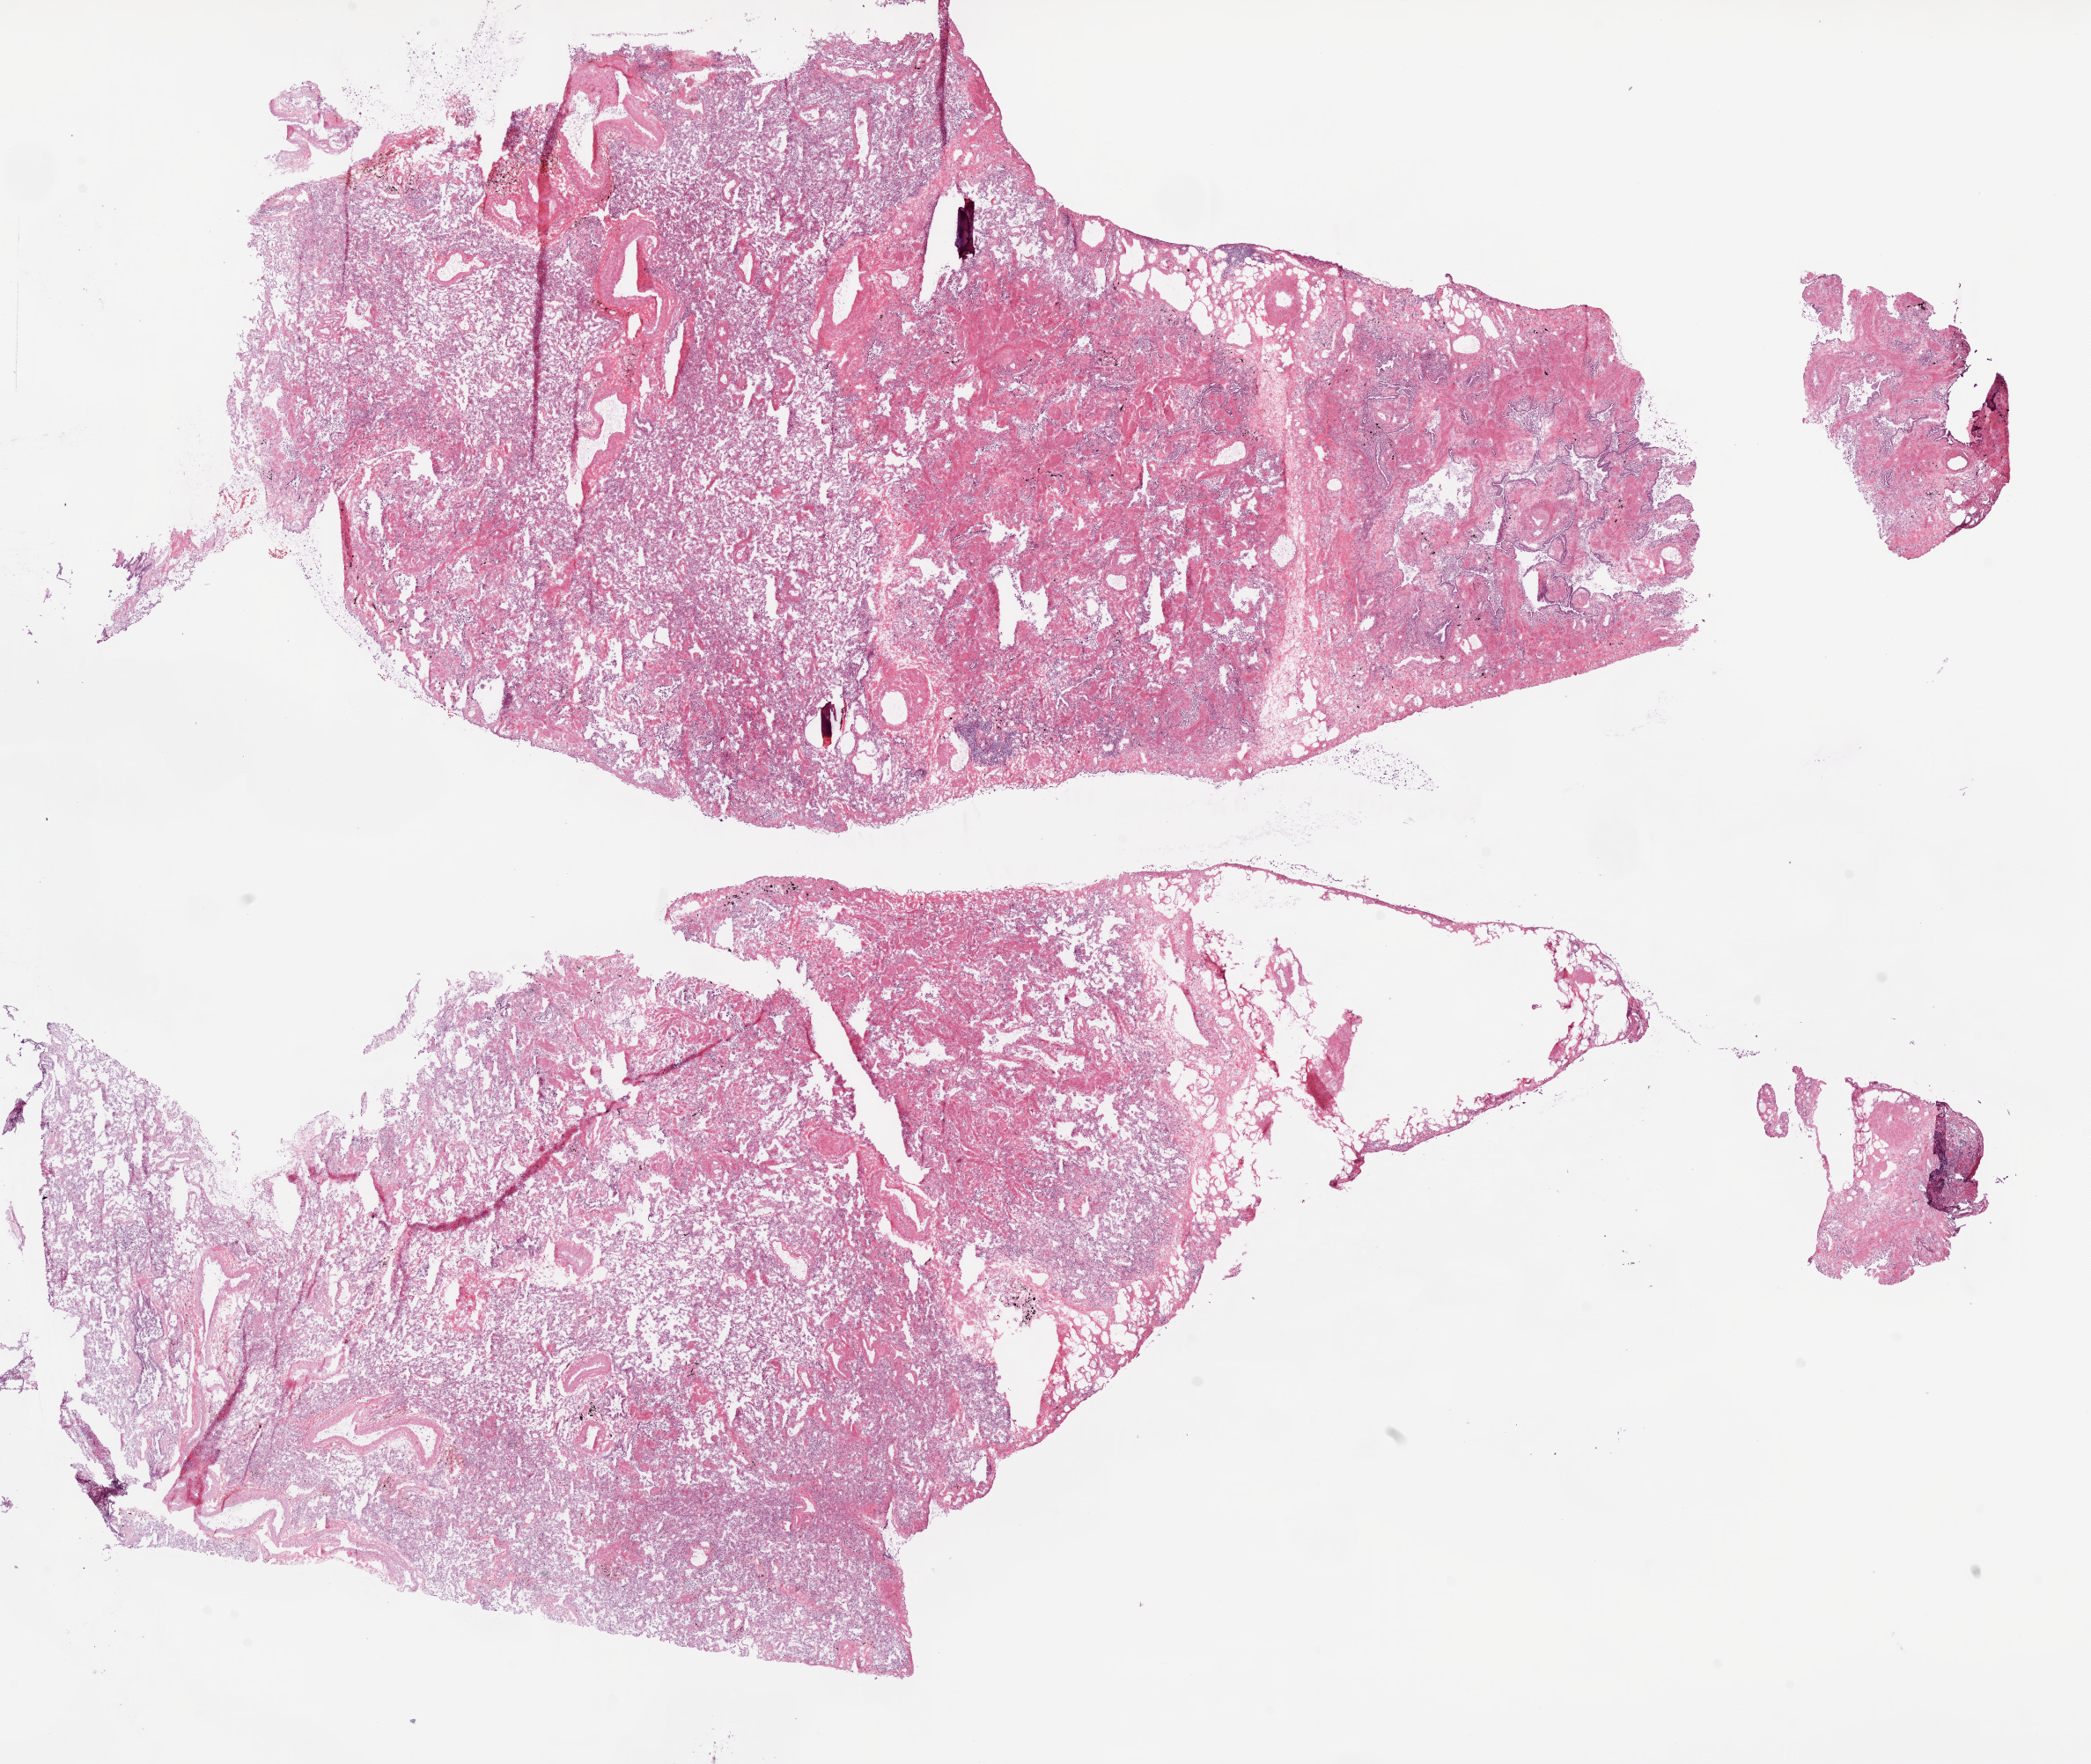
Hematoxylin and eosin (H&E) stained whole-slide image, whole scanned area (about 19.1 x 16.1 mm, from a 20x scan) shown as a low-resolution overview; frozen section from the top of the tissue portion; solid tissue normal (non-tumour tissue) sample from the lung. Male, age 76 years at initial diagnosis.
* this section: solid tissue normal sample (biorepository sample class)
* patient diagnosis: Squamous cell carcinoma, NOS (upper lobe, lung)